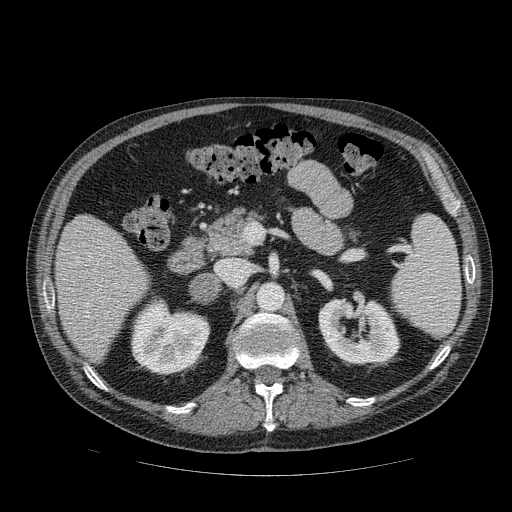
Contrast-enhanced abdominal CT, one axial slice. Slice 46 of 111 in the series (ordered by position). Intravenous contrast given. Soft-tissue window (W 400 / L 40 HU). 2.5 mm slice thickness. 512 × 512 image matrix, field of view 420 × 420 mm. Patient: male, 56 years. From the clinical record (not read from this slice): diagnosis: adrenocortical carcinoma; tumour side: right adrenal; tumour size at pathology: 9 cm; Ki-67 index: 48 %; stage (as recorded): 4.
Structures marked on this image (semi-automatic segmentation, software-assisted and operator-edited):
- mass: bounding box <190,275,218,301> (left, top, right, bottom; pixels)